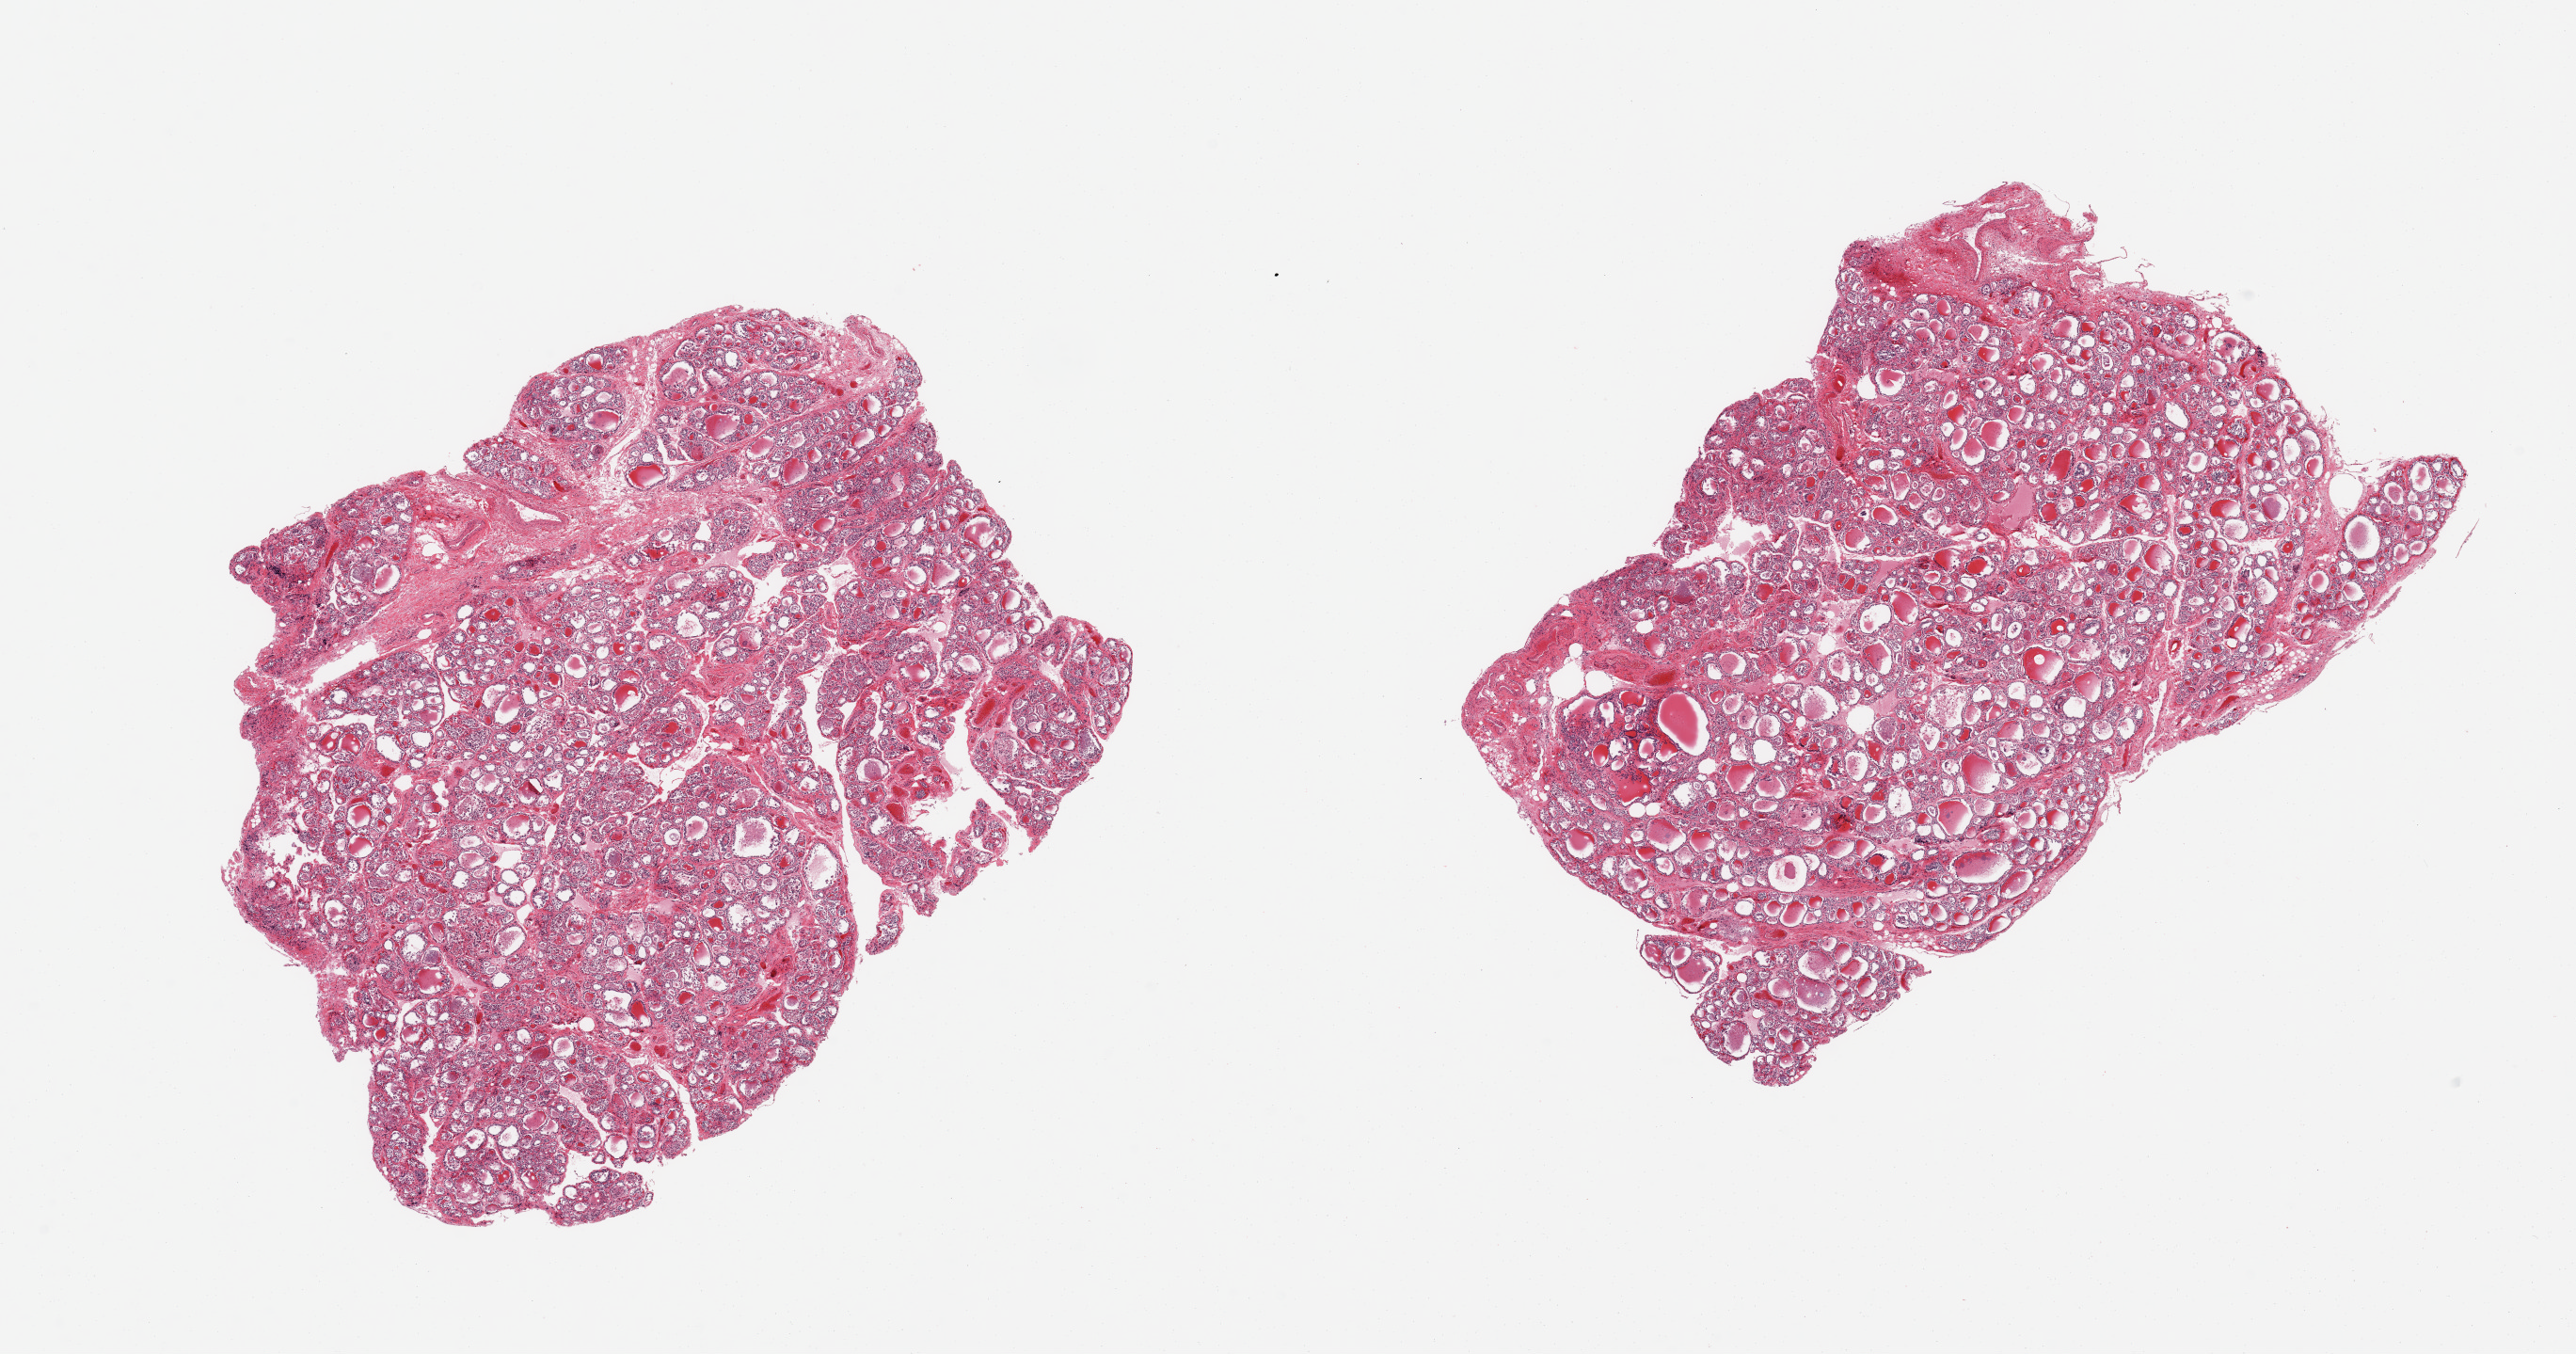
H&E whole-slide image, brightfield, whole scanned area (about 21.7 x 11.4 mm, slide scanned at 20x) shown as a low-resolution overview, PAXgene-fixed paraffin-embedded (PFPE) section, sampled site (target tissue): thyroid, tissue donor sample. Male donor.
Reviewer comment on this tissue sample: 2 pieces; mild fibrosis with vague nodularity.